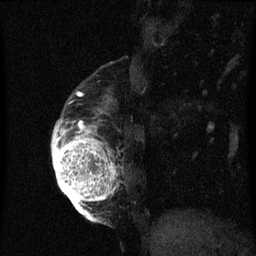
Breast MRI (dynamic contrast-enhanced), one sagittal slice. Position 15 of 60 along the scan axis. Dynamic contrast-enhanced series, image 2 of 3 at this slice position (ordered by acquisition). 1.5 T. TE 4.2 ms, TR 8 ms. 2 mm slice thickness. 256 × 256 image matrix. Female patient, age 56 years.
Annotated regions visible in this slice (semi-automatic segmentation, software-assisted and operator-edited):
- analysis volume of interest (the breast-tissue region the enhancement analysis was run in; not a lesion): bounding box [x1, y1, x2, y2] px = [52, 96, 123, 219]
- tumour enhancement mask (voxels above the 70 % enhancement threshold inside the analysis volume of interest): [52, 122, 117, 219]